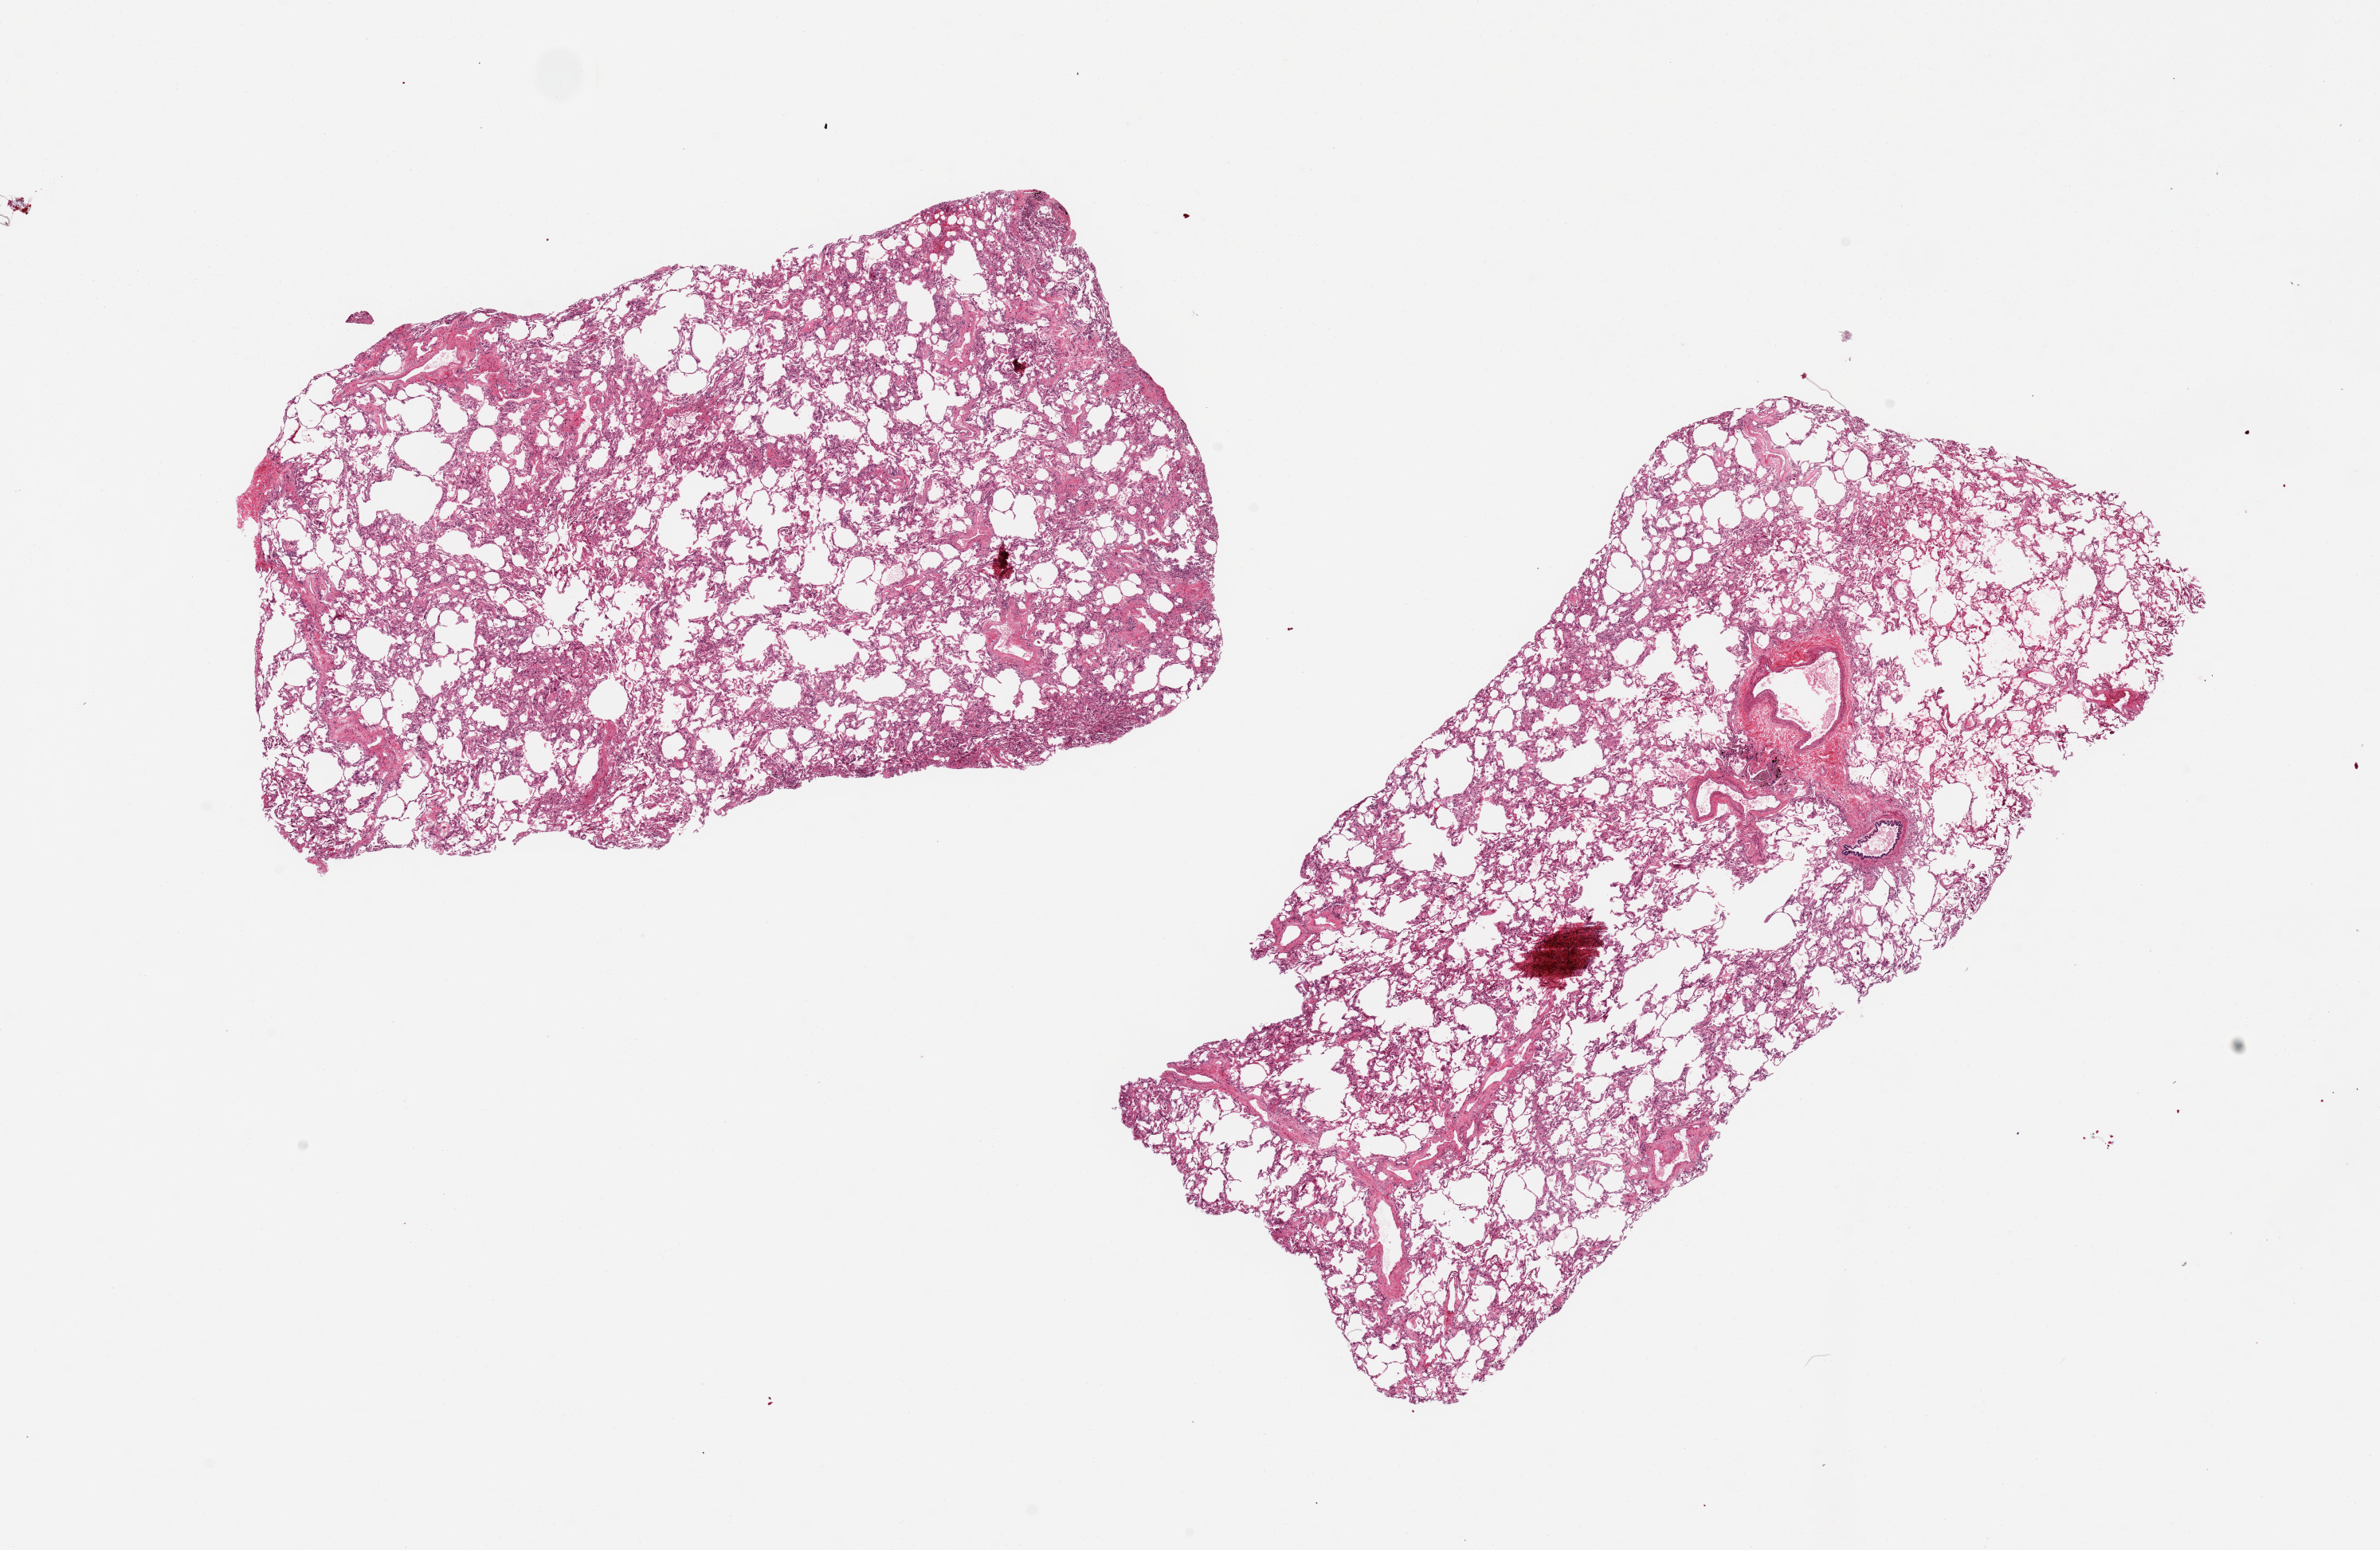
Whole-slide image, H&E stain — low-resolution overview of the scanned area, about 23.6 x 15.4 mm (from a 20x scan). PAXgene-fixed, paraffin-embedded tissue. Section of lung (target tissue). Donor tissue sample. Donor sex: female.
Review note (as recorded): 2 aliquots, ~9x5mm. Patchy mild edema, a few hyaline membranes.